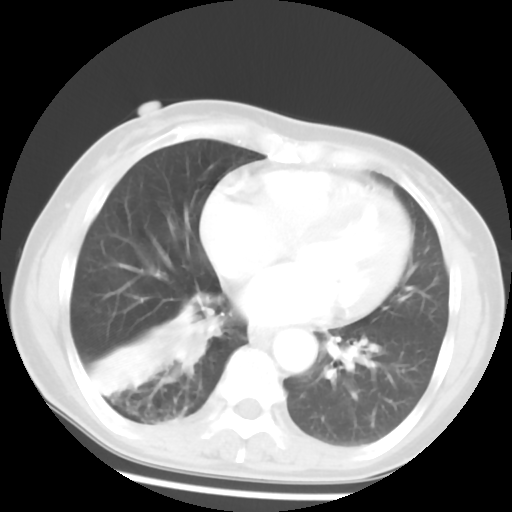
Chest CT, one axial slice. Slice 22 of 52 in the series (ordered by position). 120 kVp. Lung window (W 1500 / L -600 HU). 5 mm slice thickness. 512 × 512 image matrix, field of view 297 × 297 mm. Female patient, age 54 years. Case-level facts recorded for this patient, not image findings: clinical TNM (as recorded): T1c N0 M0.
Outlined on this slice (rectangle marked by the reading radiologist):
- lung tumour (recorded histology: squamous cell carcinoma): bounding box (x1, y1, x2, y2) in pixels: (163, 297, 223, 373)